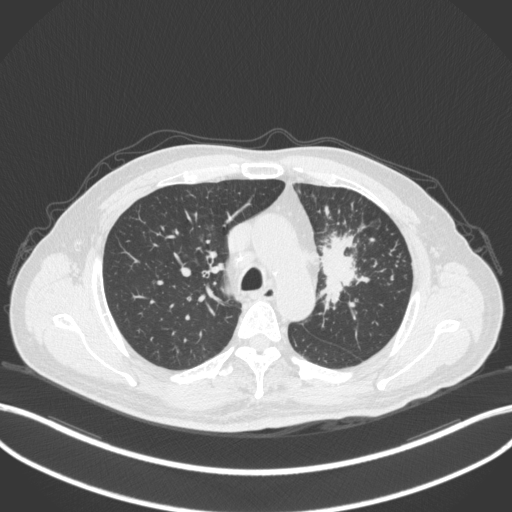
Chest CT, one axial slice; 120 kVp; lung window (W 1500 / L -600 HU); 1 mm slice thickness; 512 × 512 image matrix, field of view 400 × 400 mm. Male patient, age 69 years. Case-level facts recorded for this patient, not image findings: clinical TNM (as recorded): T2a N2 M0.
Annotated regions visible in this slice (bounding box drawn by a radiologist):
- lung tumour (recorded histology: adenocarcinoma): box from (x=318, y=225) to (x=372, y=315) px